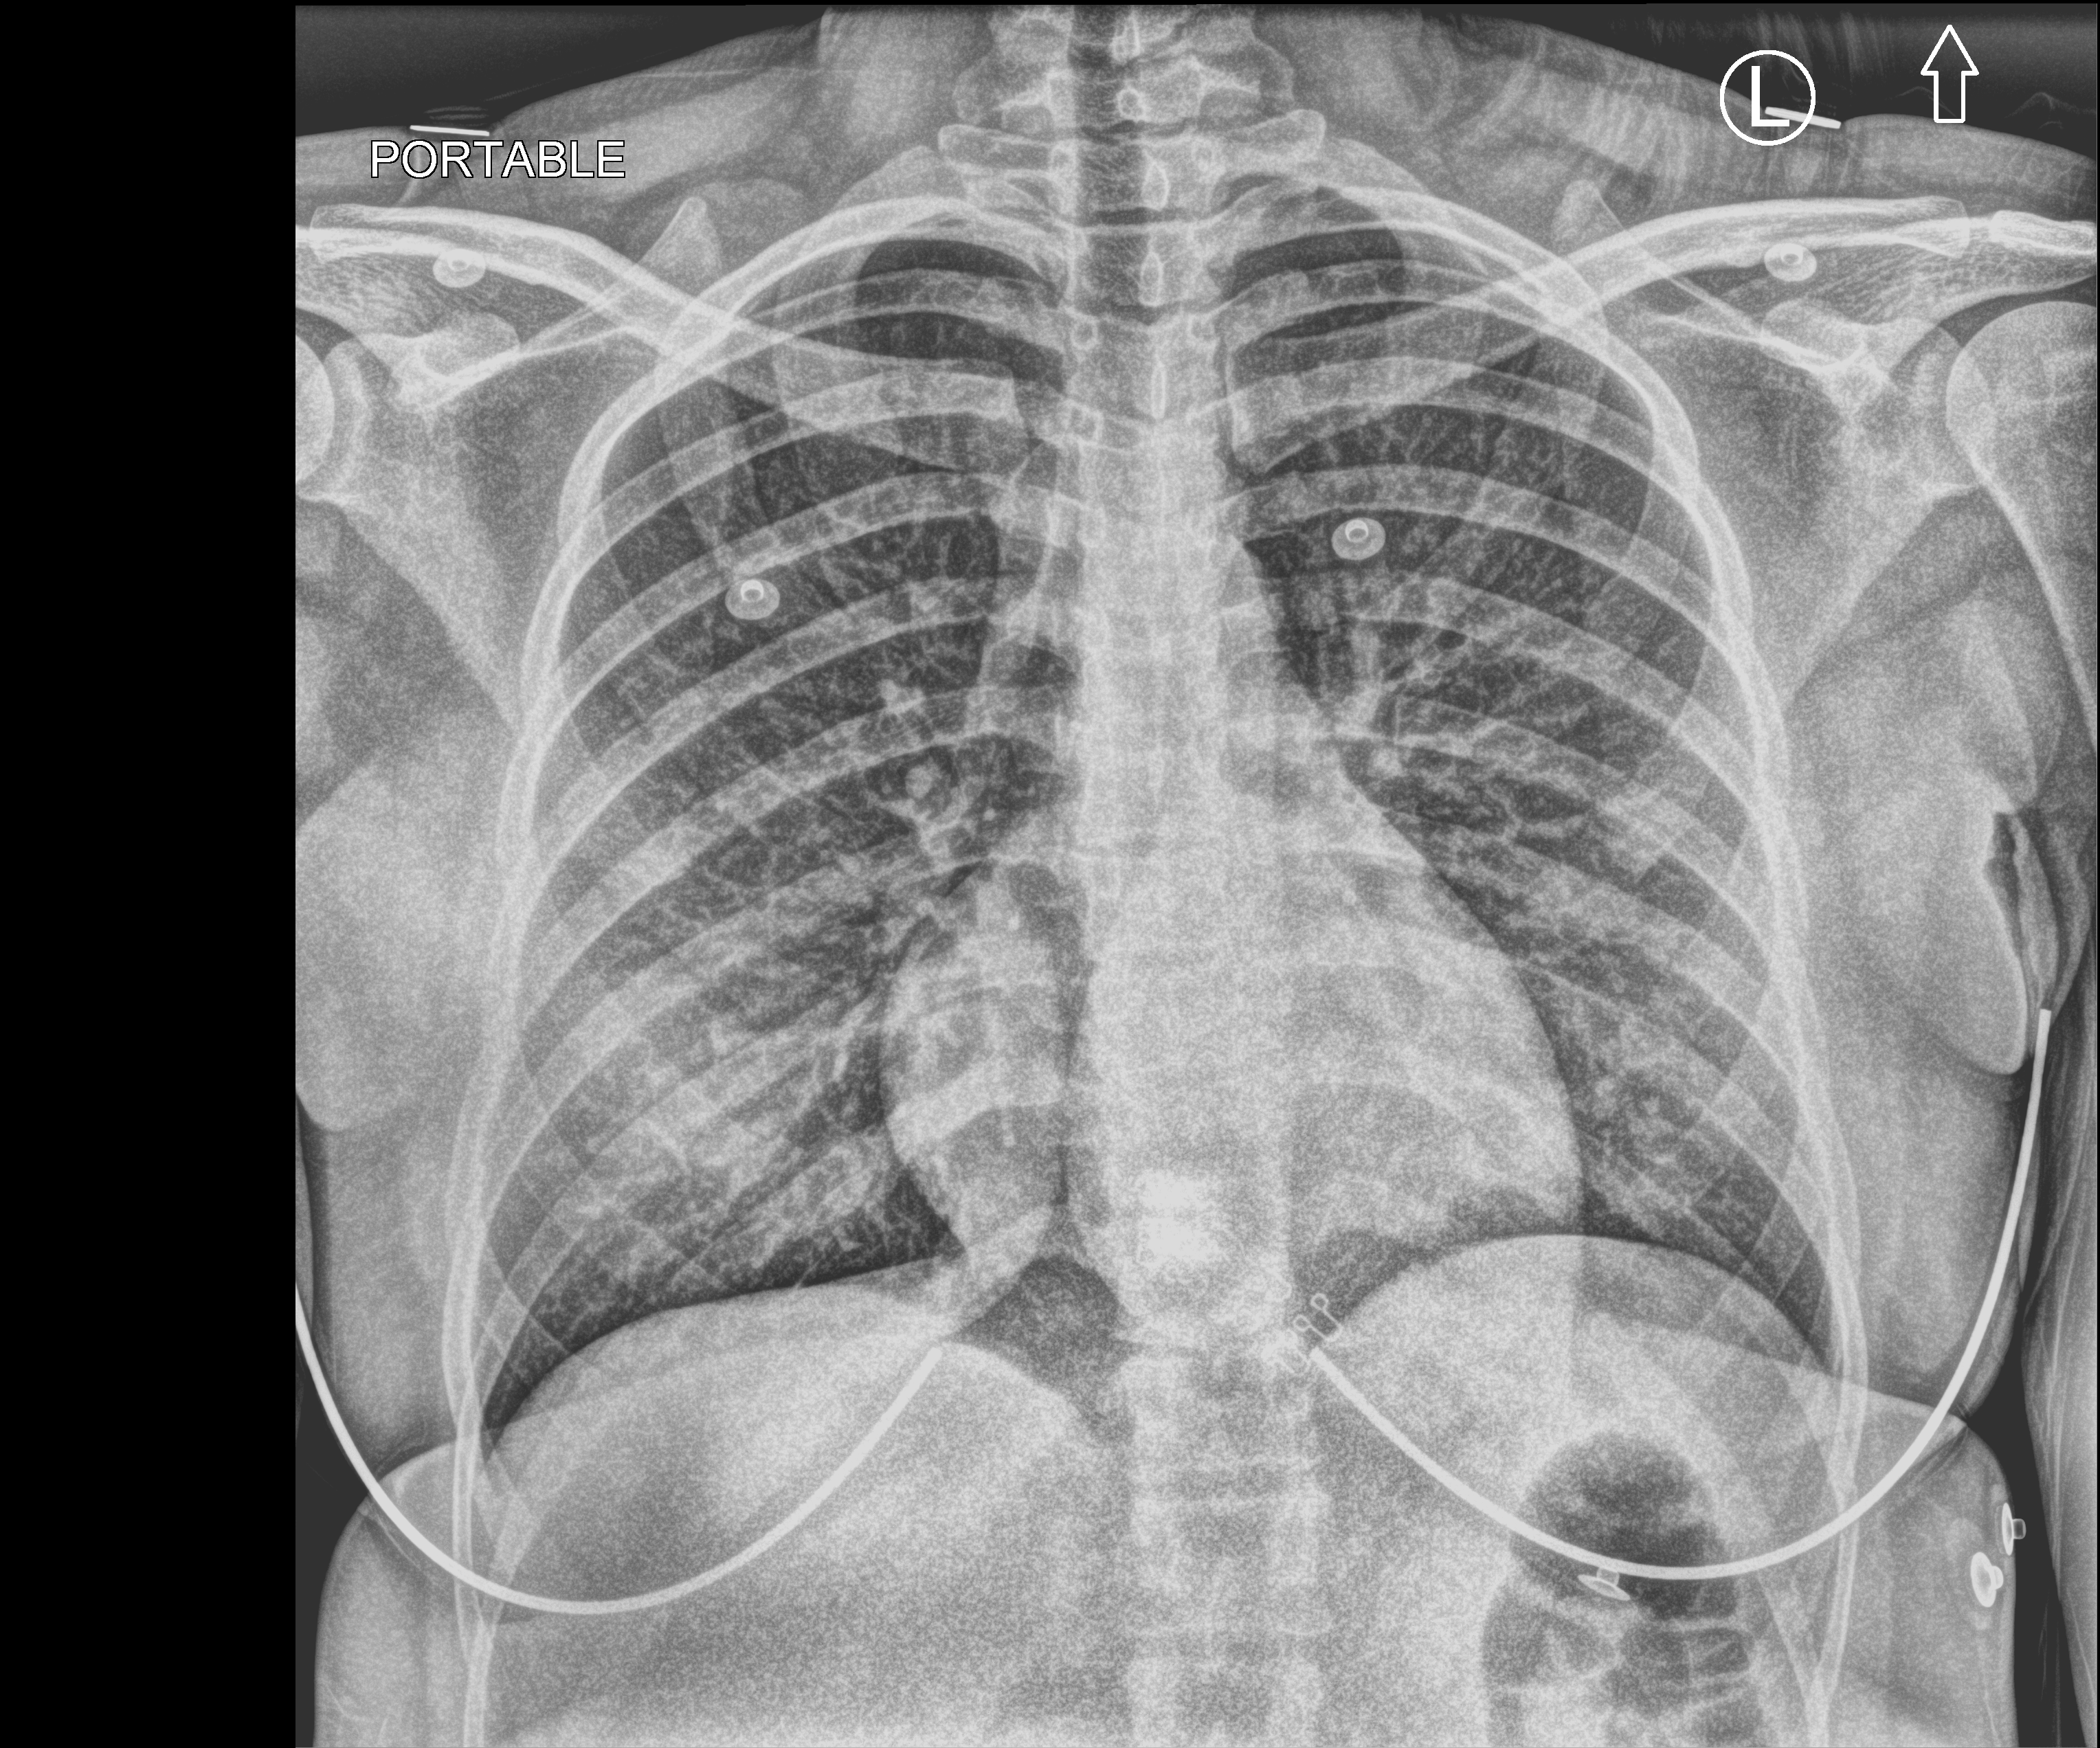
Bedside chest radiograph (computed radiography); anteroposterior (AP) projection. Female patient hospitalised with COVID-19, age 18–59 years.
Hospital-stay facts (about this admission, not read from this image; timing relative to this image not recorded):
- admitted to intensive care during this hospital stay: no